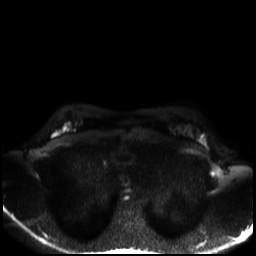
Breast MRI, one axial slice; position 21 of 30 along the scan axis; diffusion-weighted series; image 2 of 4 stored at this slice position (different b-values; order by instance number); 3 T; 256 × 256 image matrix, field of view 320 × 320 mm. Female patient.
Annotated regions visible in this slice (outlined manually by an expert reader):
- tumour on diffusion-weighted imaging: bounding box <196,136,205,144> (left, top, right, bottom; pixels)